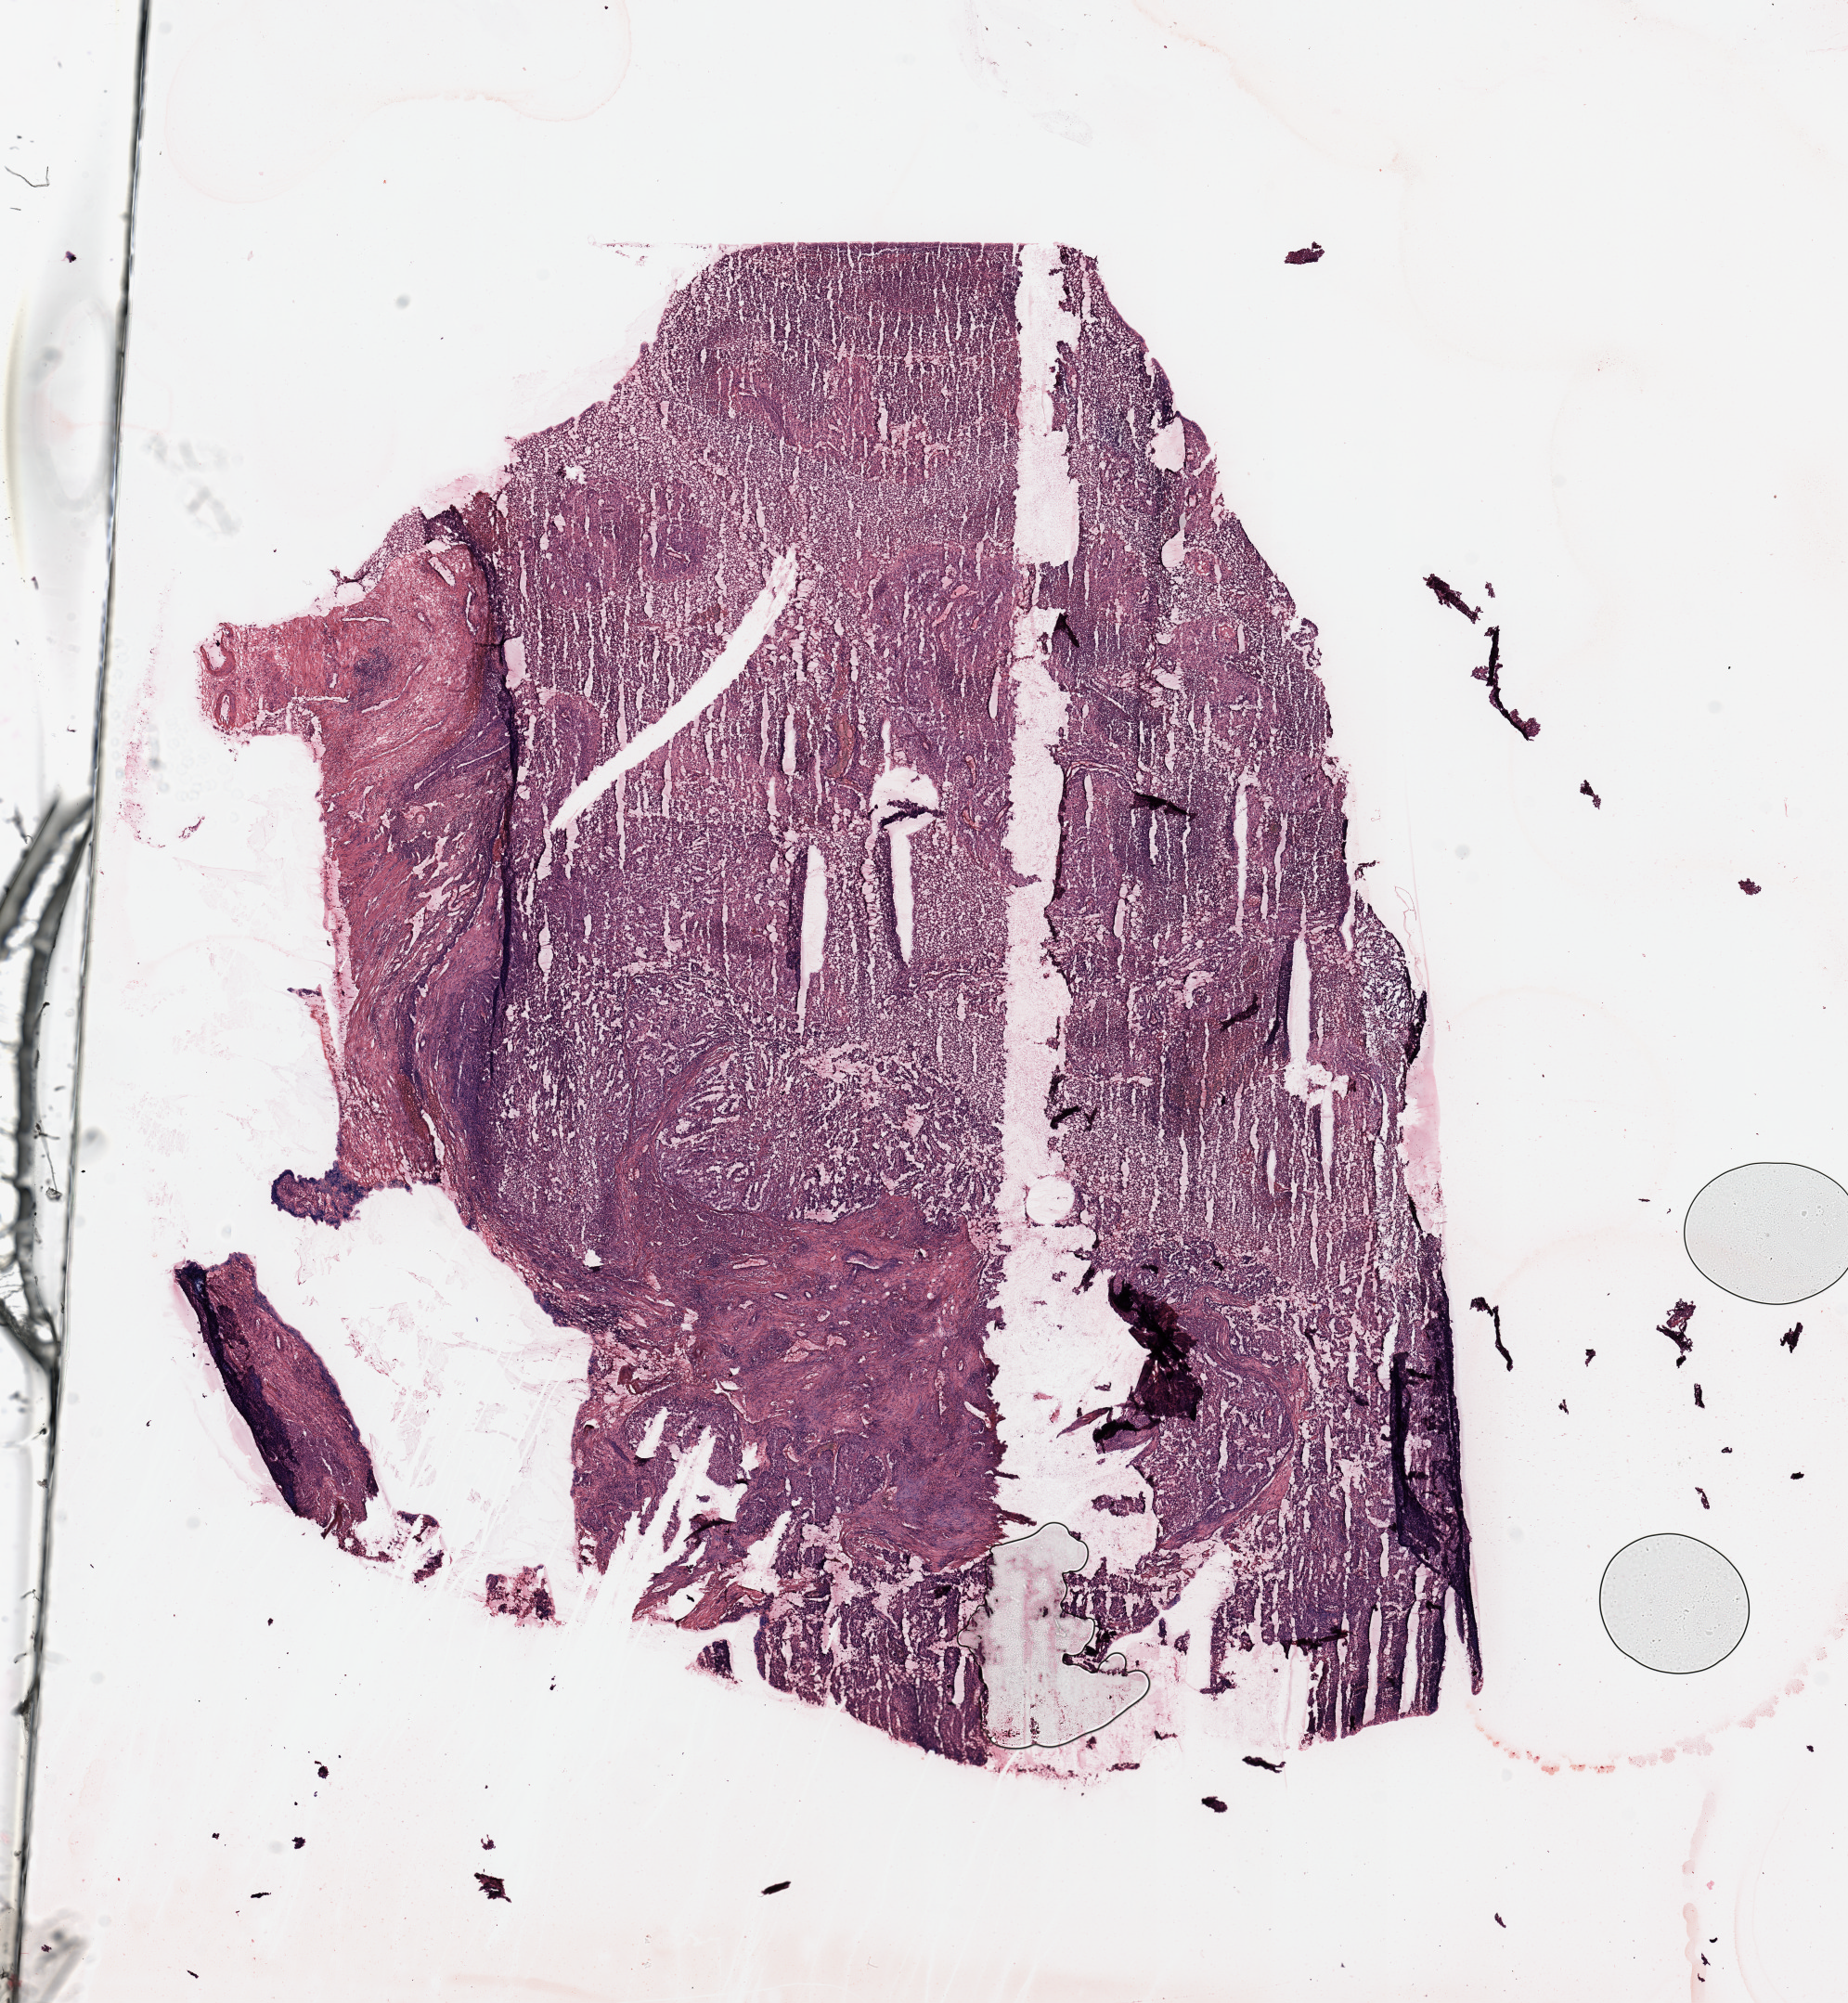
Digitized Hematoxylin and eosin (H&E) stained tissue section (whole slide), whole scanned area (about 15.8 x 17.1 mm, slide scanned at 20x) shown as a low-resolution overview, tumour tissue sample, kidney. Male, 72 y/o. Histologic grade: G3 (poorly differentiated).
AJCC pathologic stage: III. Histologic diagnosis: Renal cell carcinoma, NOS. Primary tumour site (as recorded): upper pole.